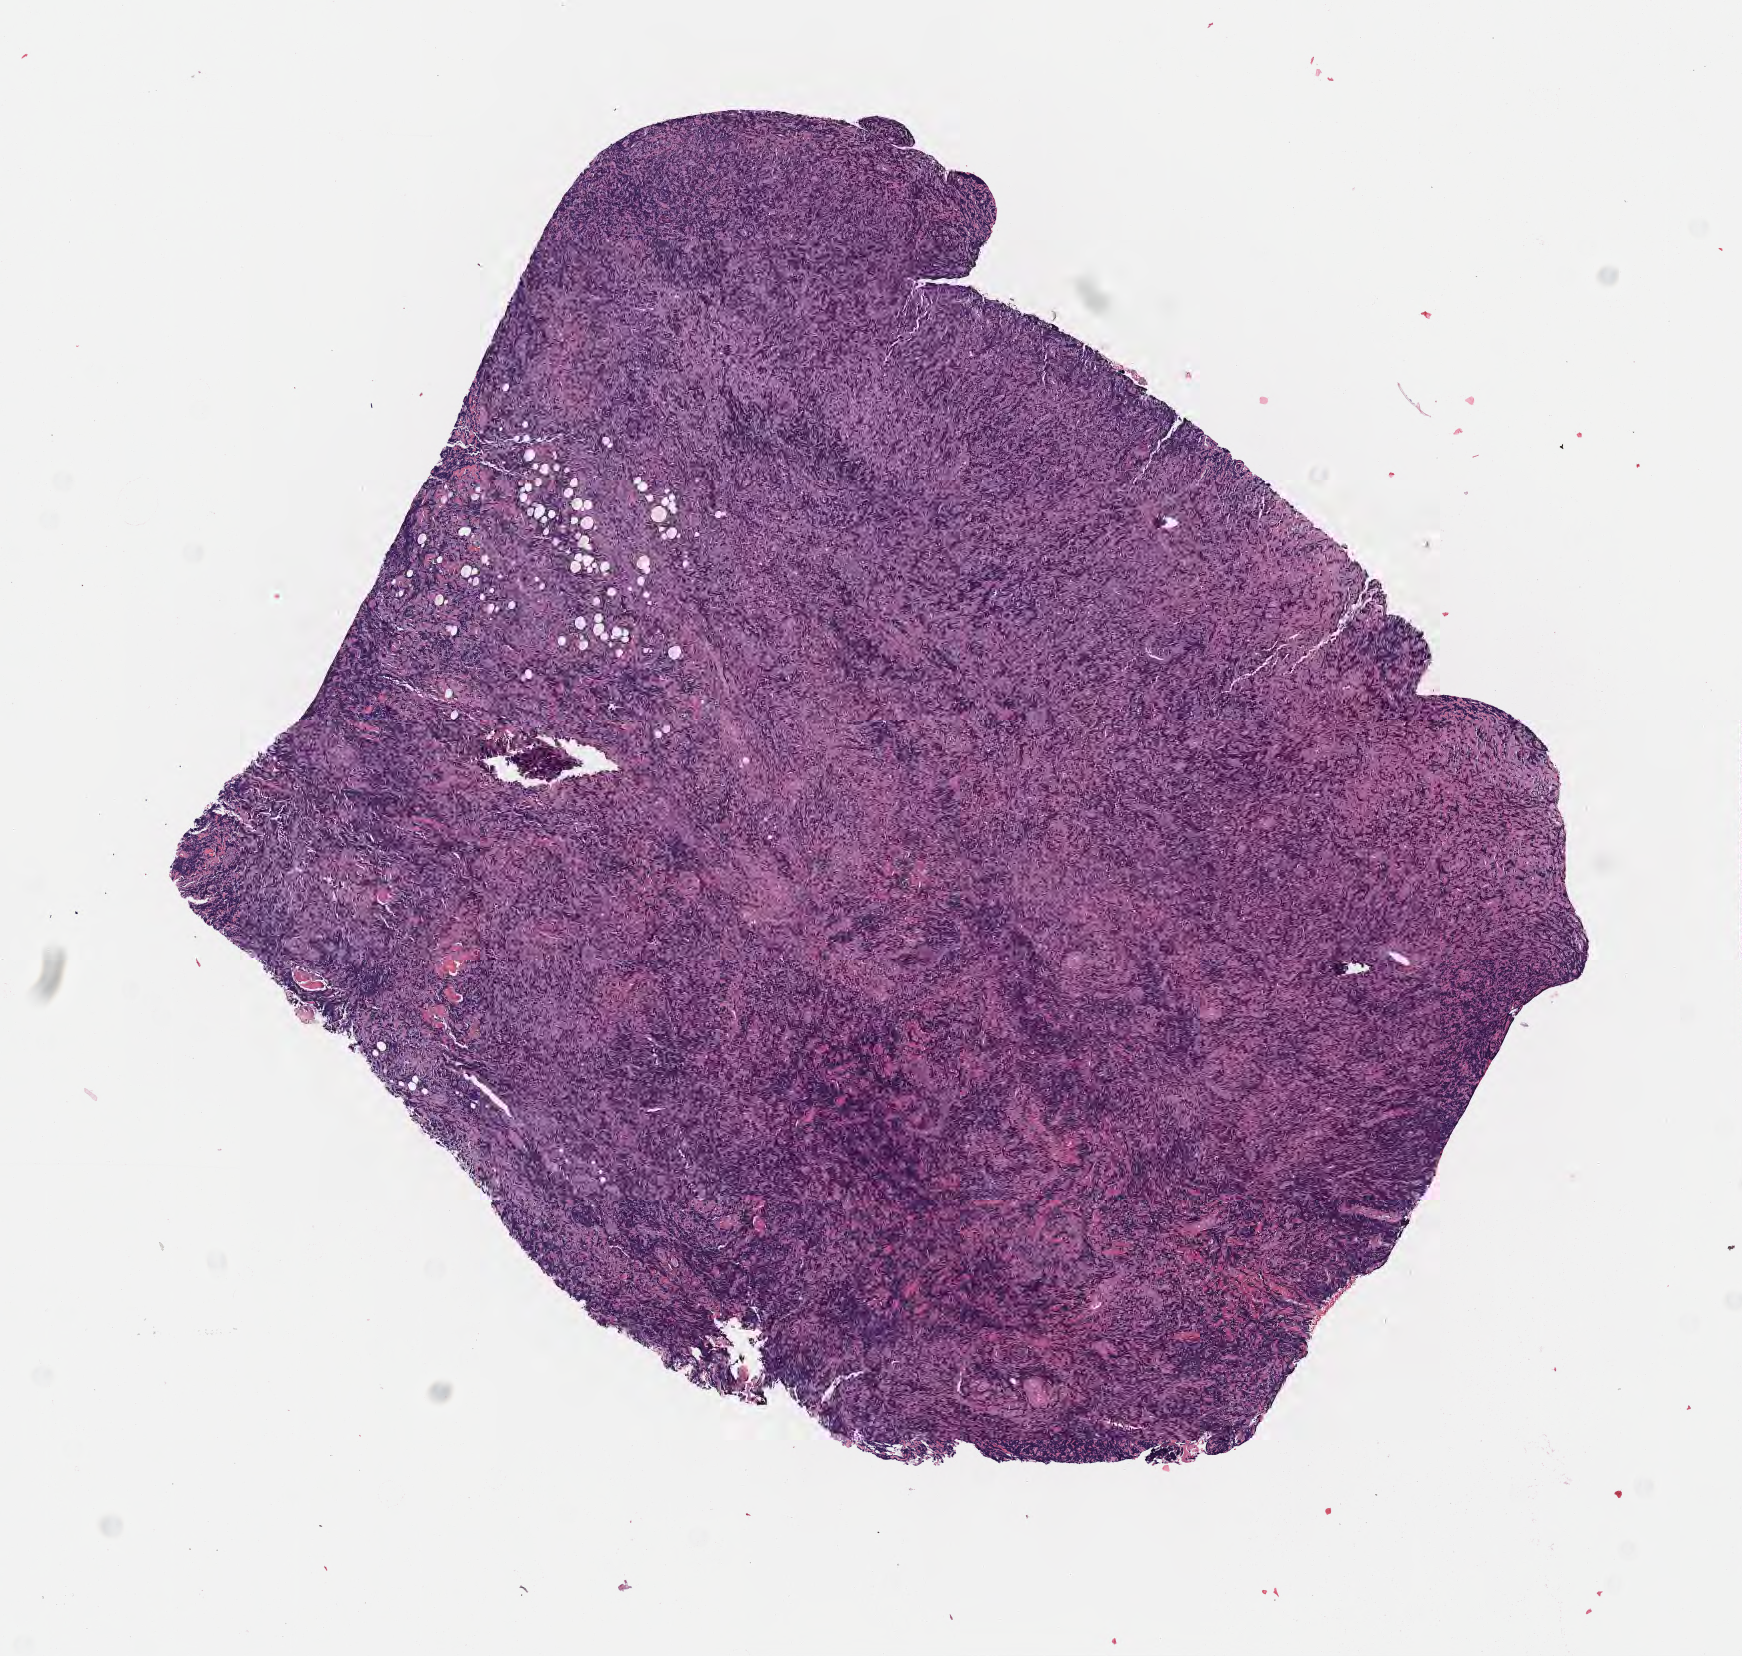
Whole-slide image, hematoxylin and eosin (H&E) stain — whole scanned area (about 7.0 x 6.7 mm) shown as a low-resolution overview, specimen: tumor tissue, anatomic site: buccal mucosa. Male, age 7 years at initial diagnosis.
* histologic diagnosis: Burkitt lymphoma, NOS